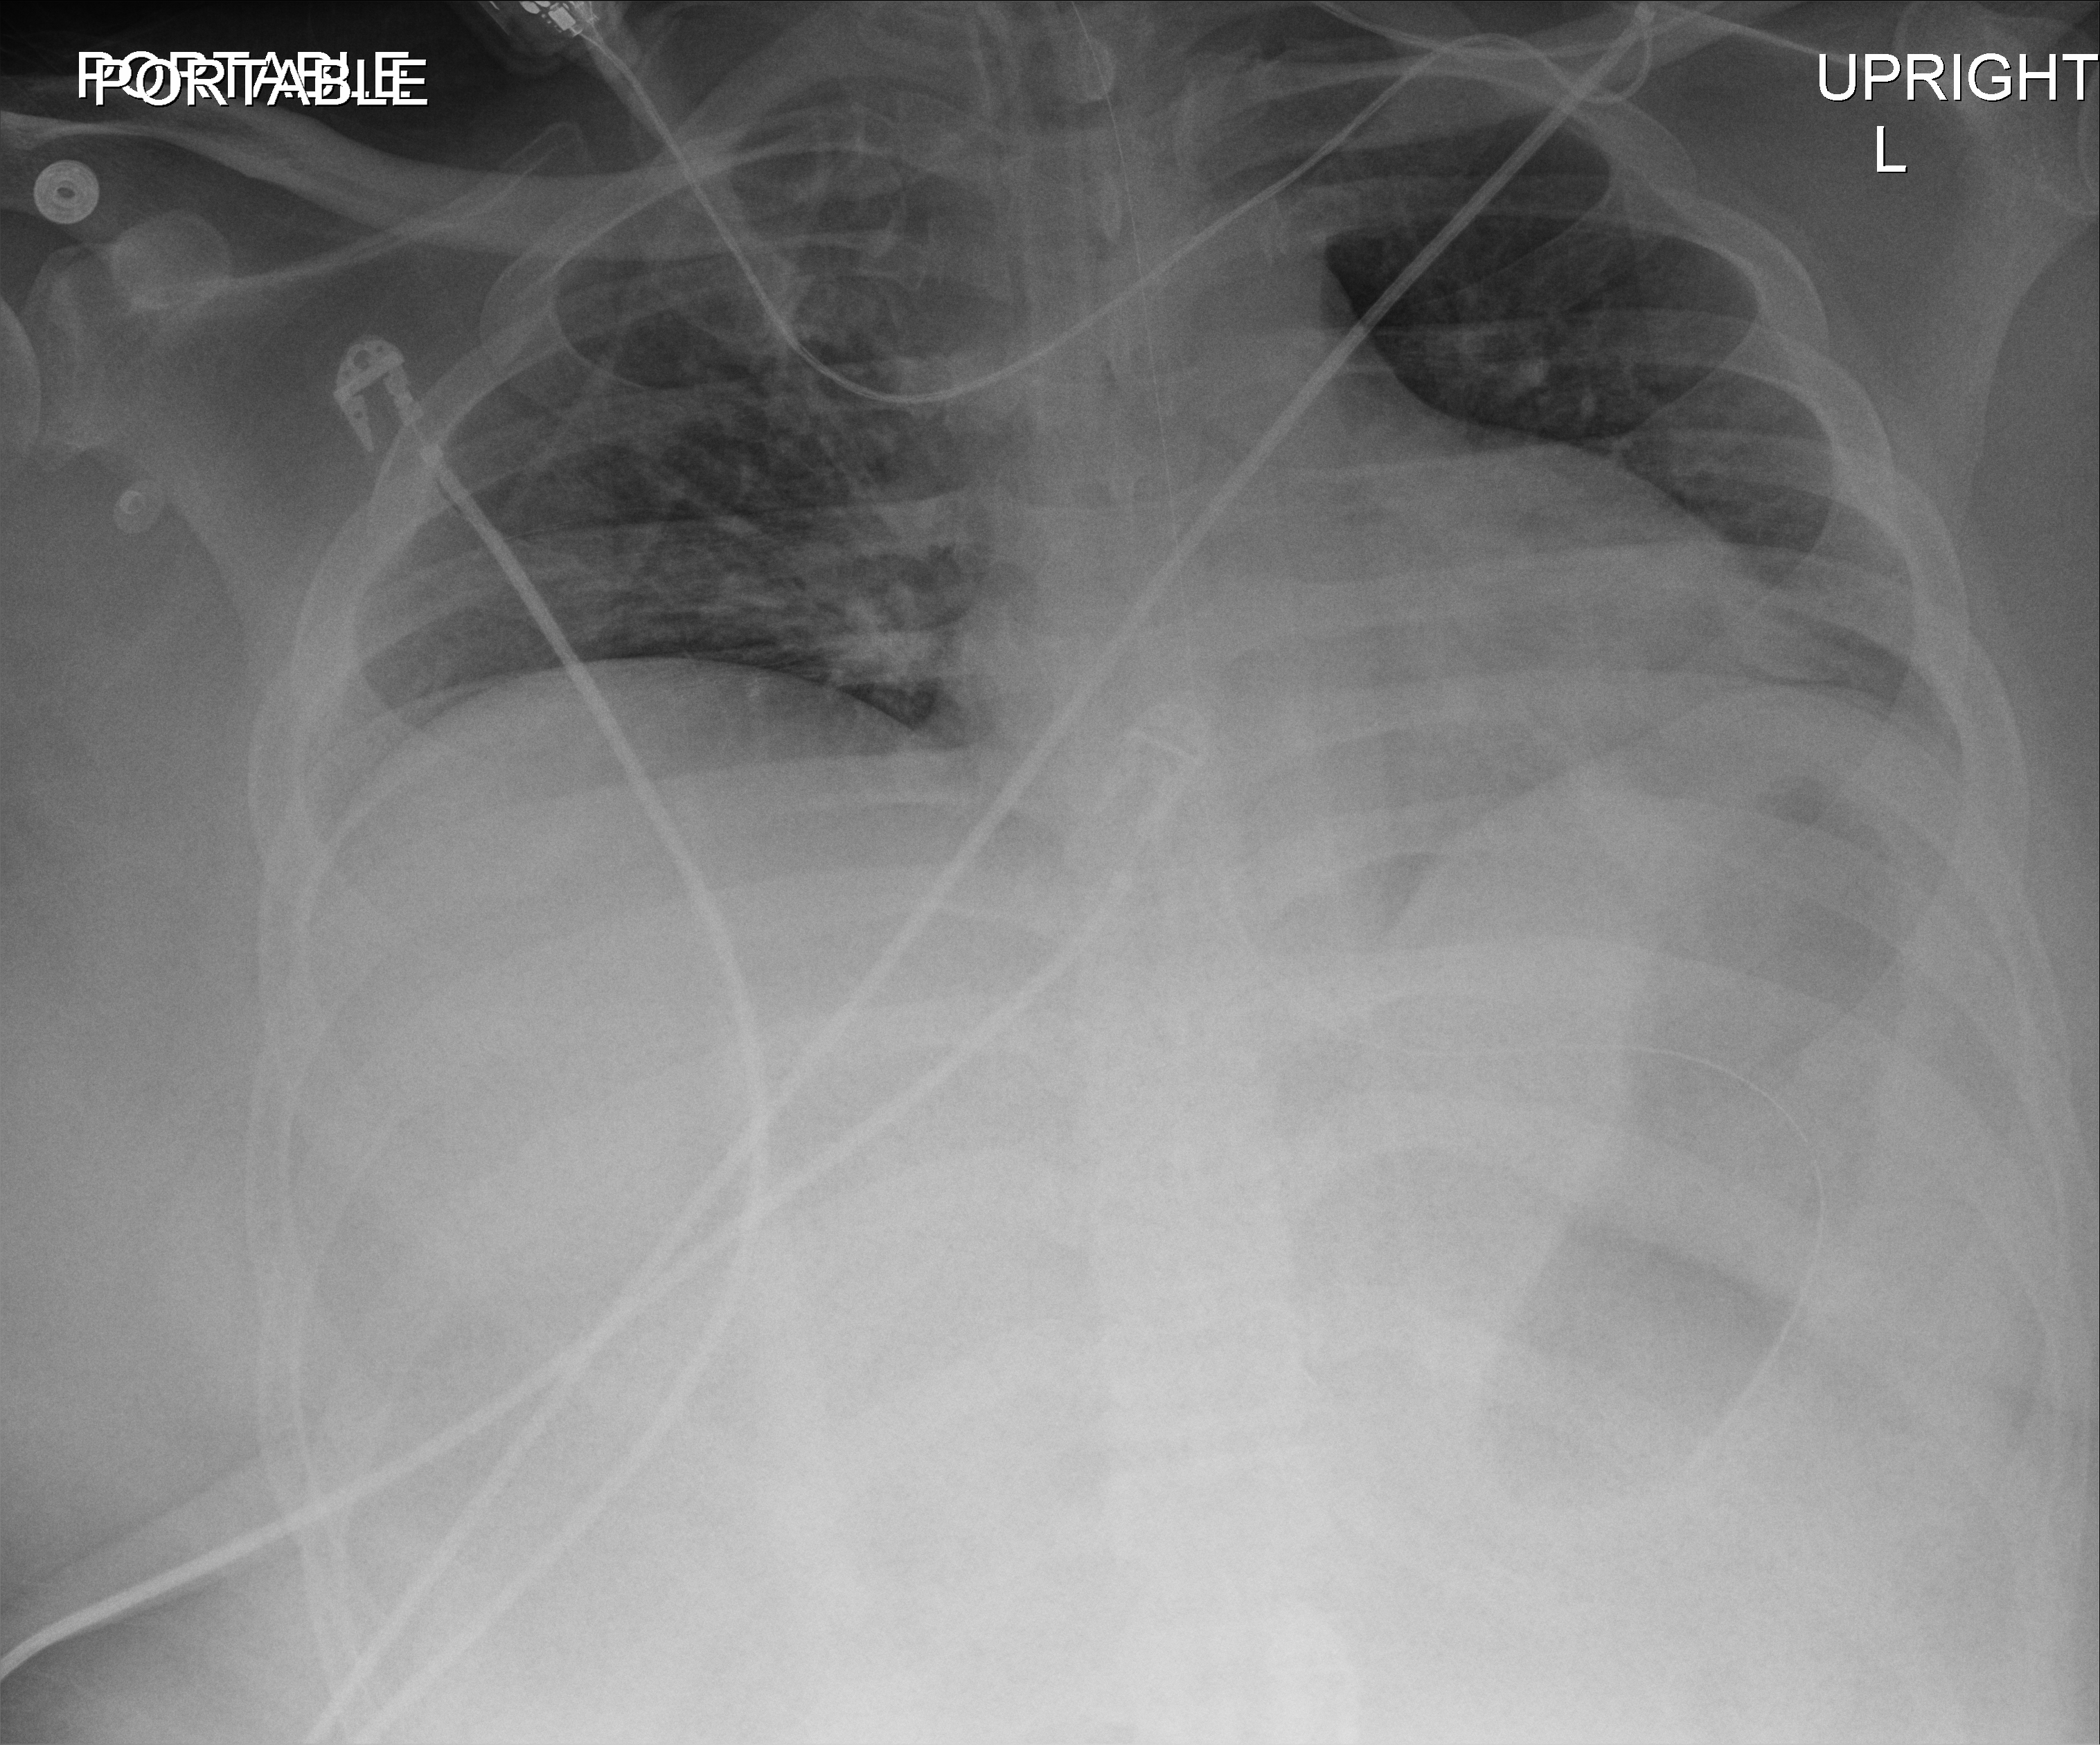
Portable chest radiograph, anteroposterior (AP) projection. Male patient hospitalised with COVID-19, age 18–59 years.
Admission-level facts for this patient (not findings on this image; timing relative to this image not recorded): admitted to intensive care during this hospital stay: yes; chronic kidney disease (admission record): no; mechanically ventilated during this hospital stay: yes.